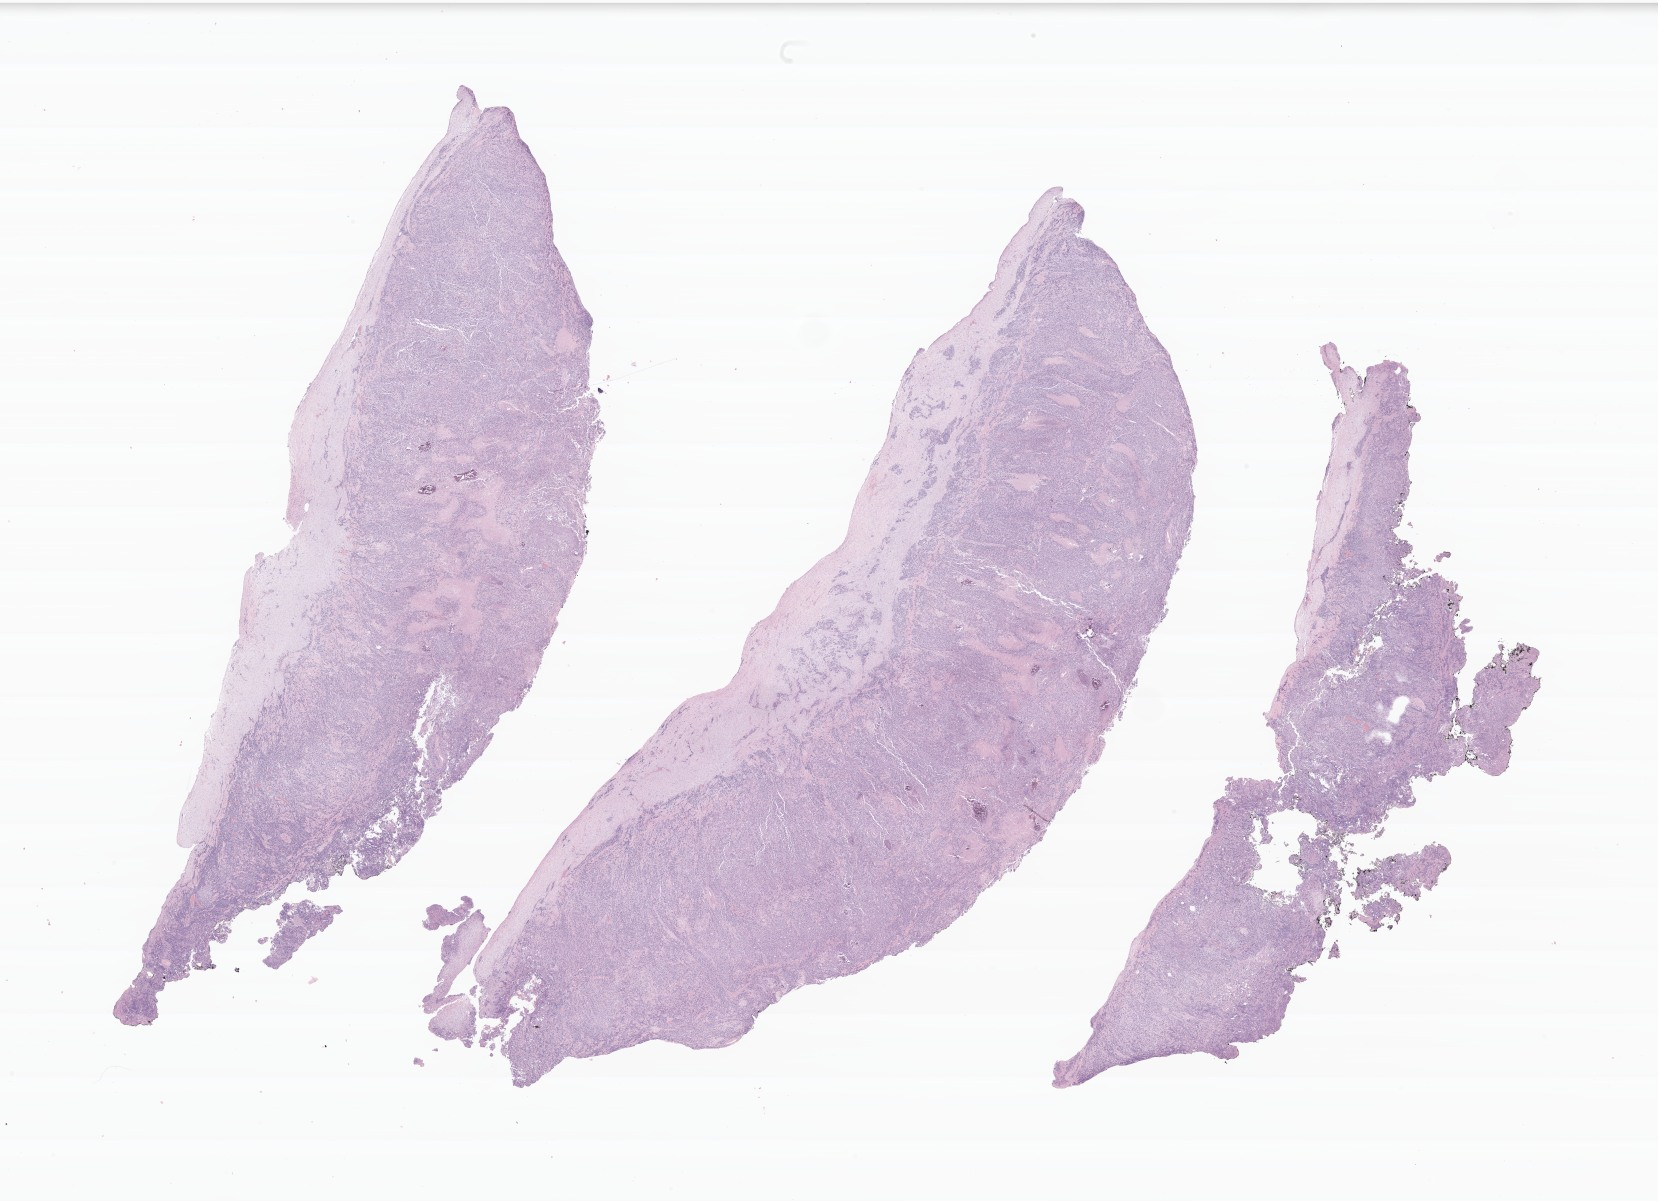
Haematoxylin and eosin whole-slide image of tumor tissue from the abdomen, a low-resolution overview of the entire scanned area, about 27.9 x 20.2 mm; formalin-fixed paraffin-embedded section. Patient: male, age 117 months (9 years 9 months).
• diagnosis: Desmoplastic small round cell tumor